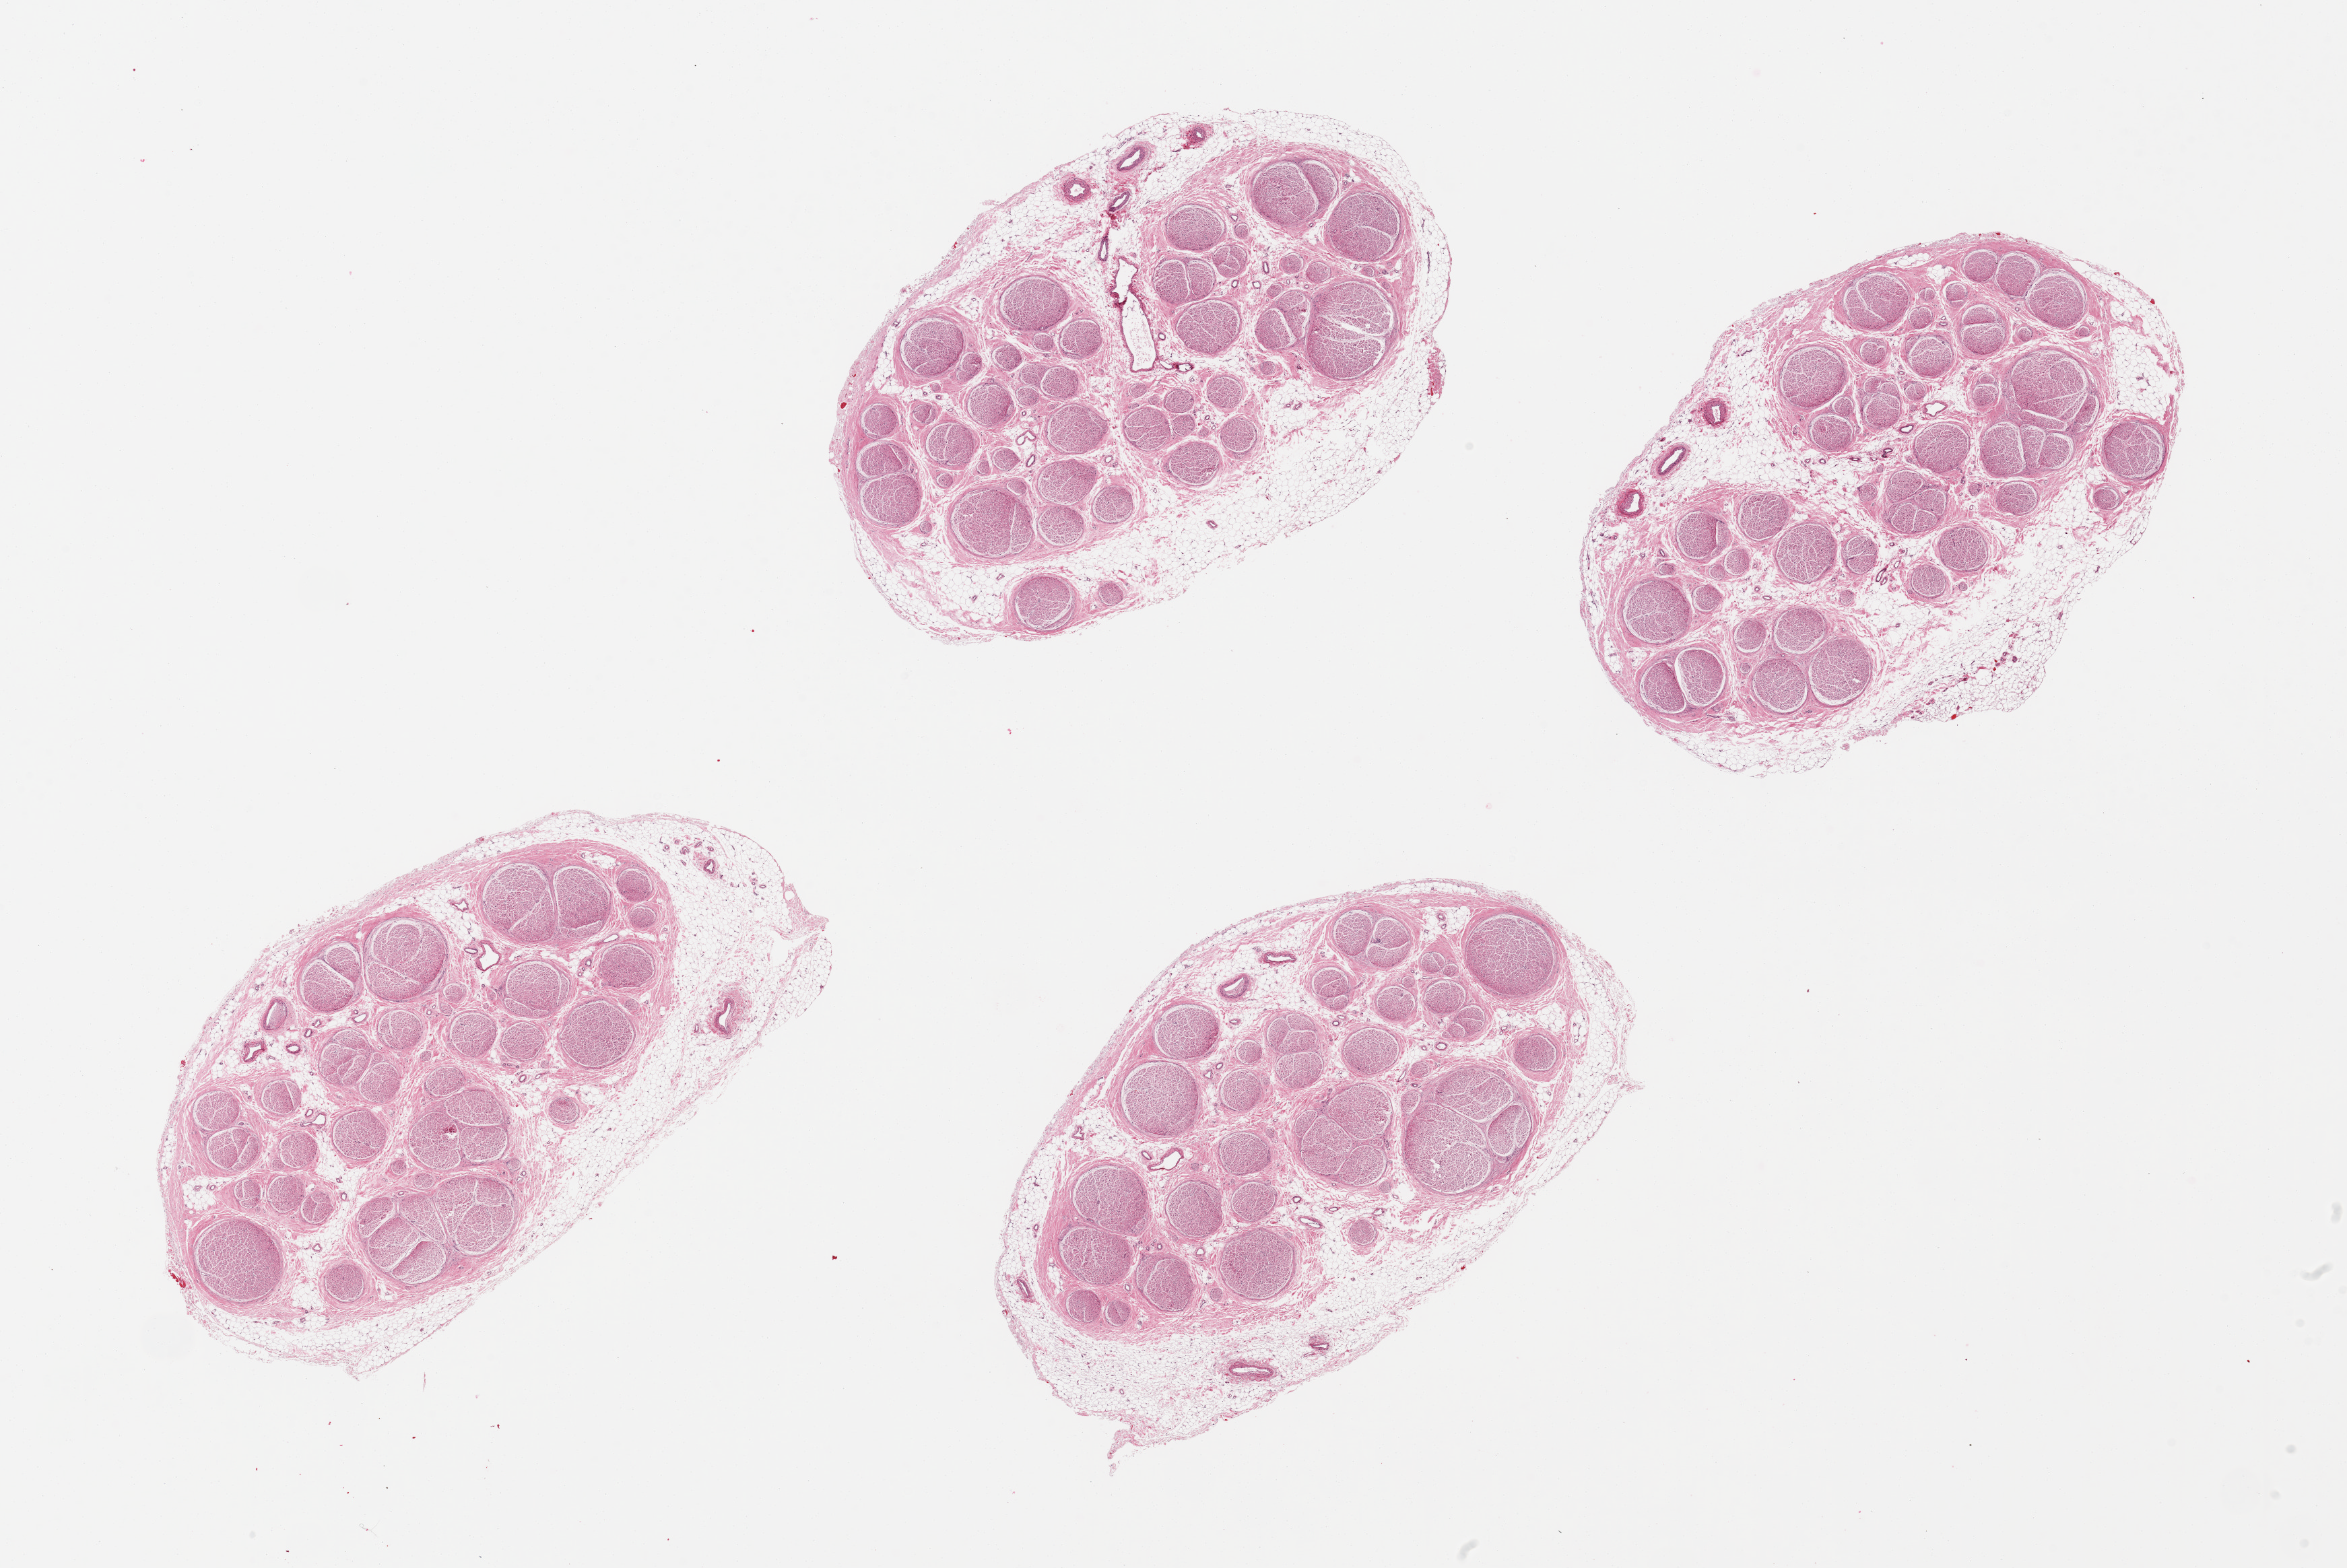
H&E whole-slide image, low-resolution overview of the scanned area, about 27.6 x 18.4 mm; PAXgene-fixed paraffin-embedded (PFPE) section; sampled site (target tissue): tibial nerve; tissue donor sample. Donor: female.
* review note (as recorded): 4 pieces, partial rims of adherent fat, 1-2mm